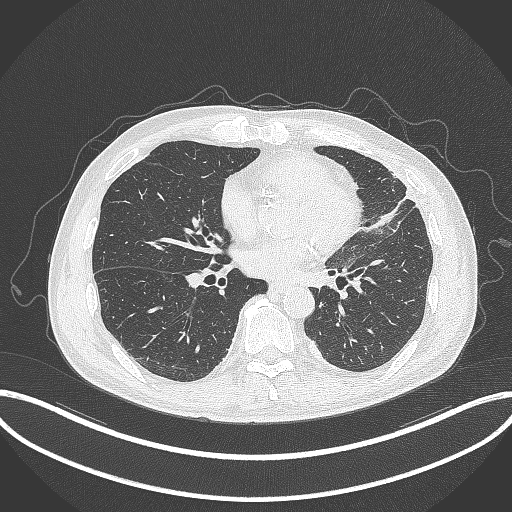
Chest CT, one axial slice; slice 143 of 382 in the series (ordered by position); lung window (W 1500 / L -600 HU); 1 mm slice thickness; 512 × 512 image matrix. Patient: male, 64 years. Case-level facts recorded for this patient, not image findings: clinical TNM (as recorded): T4 N1 M0.
Structures marked on this image (rectangle marked by the reading radiologist):
- lung tumour (recorded histology: adenocarcinoma): bounding box (x1, y1, x2, y2) in pixels: (363, 198, 415, 231)